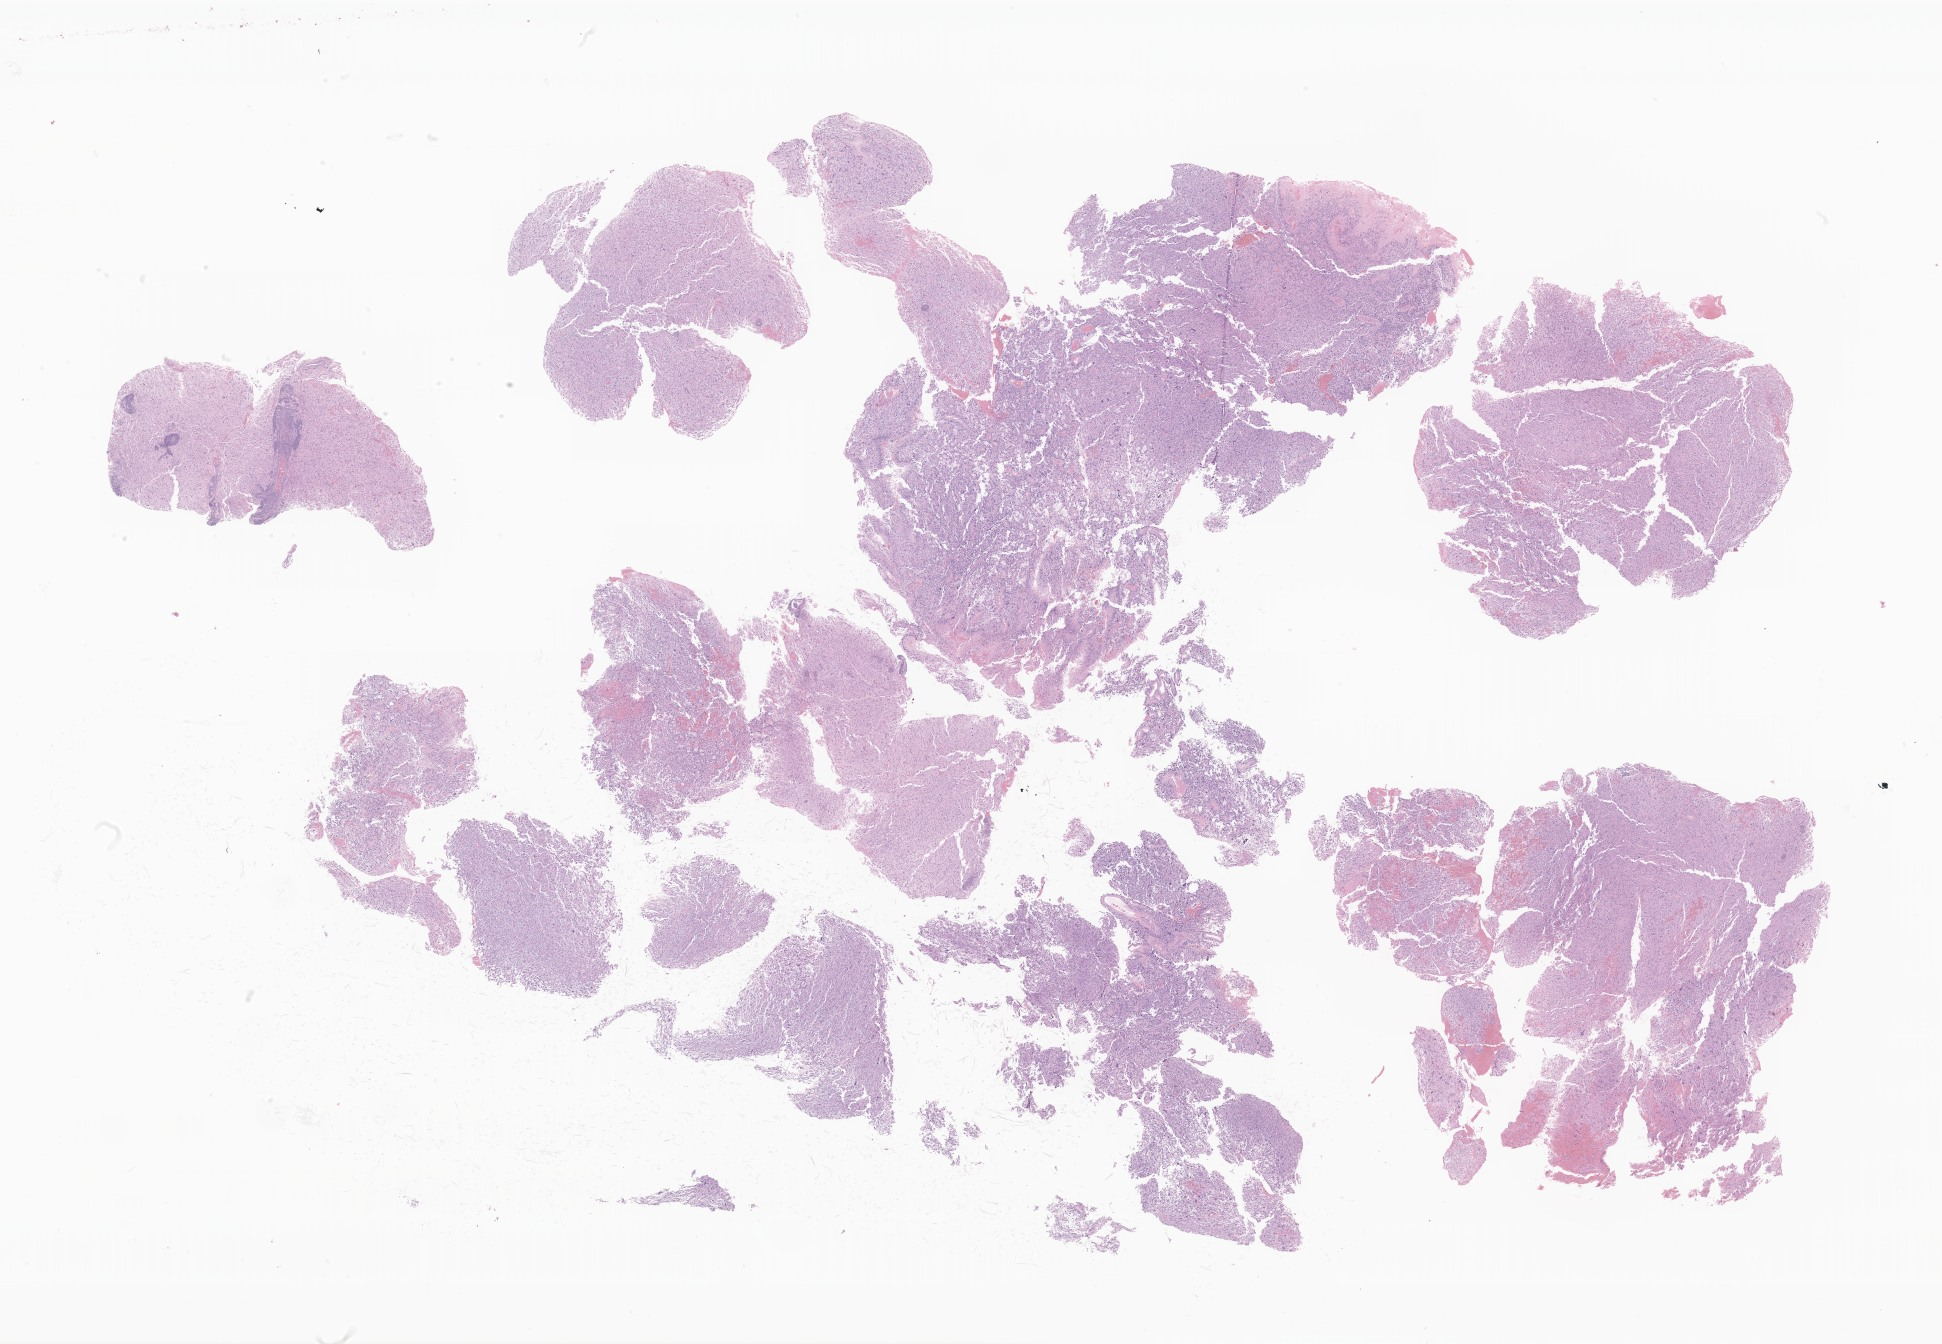
H&E whole-slide image of tumor tissue from the frontal lobe — low-resolution overview of the scanned area, about 32.8 x 22.7 mm. Formalin-fixed paraffin-embedded section. Female patient, age 274 months (22 years 10 months).
Diagnosis: Glioma, malignant.